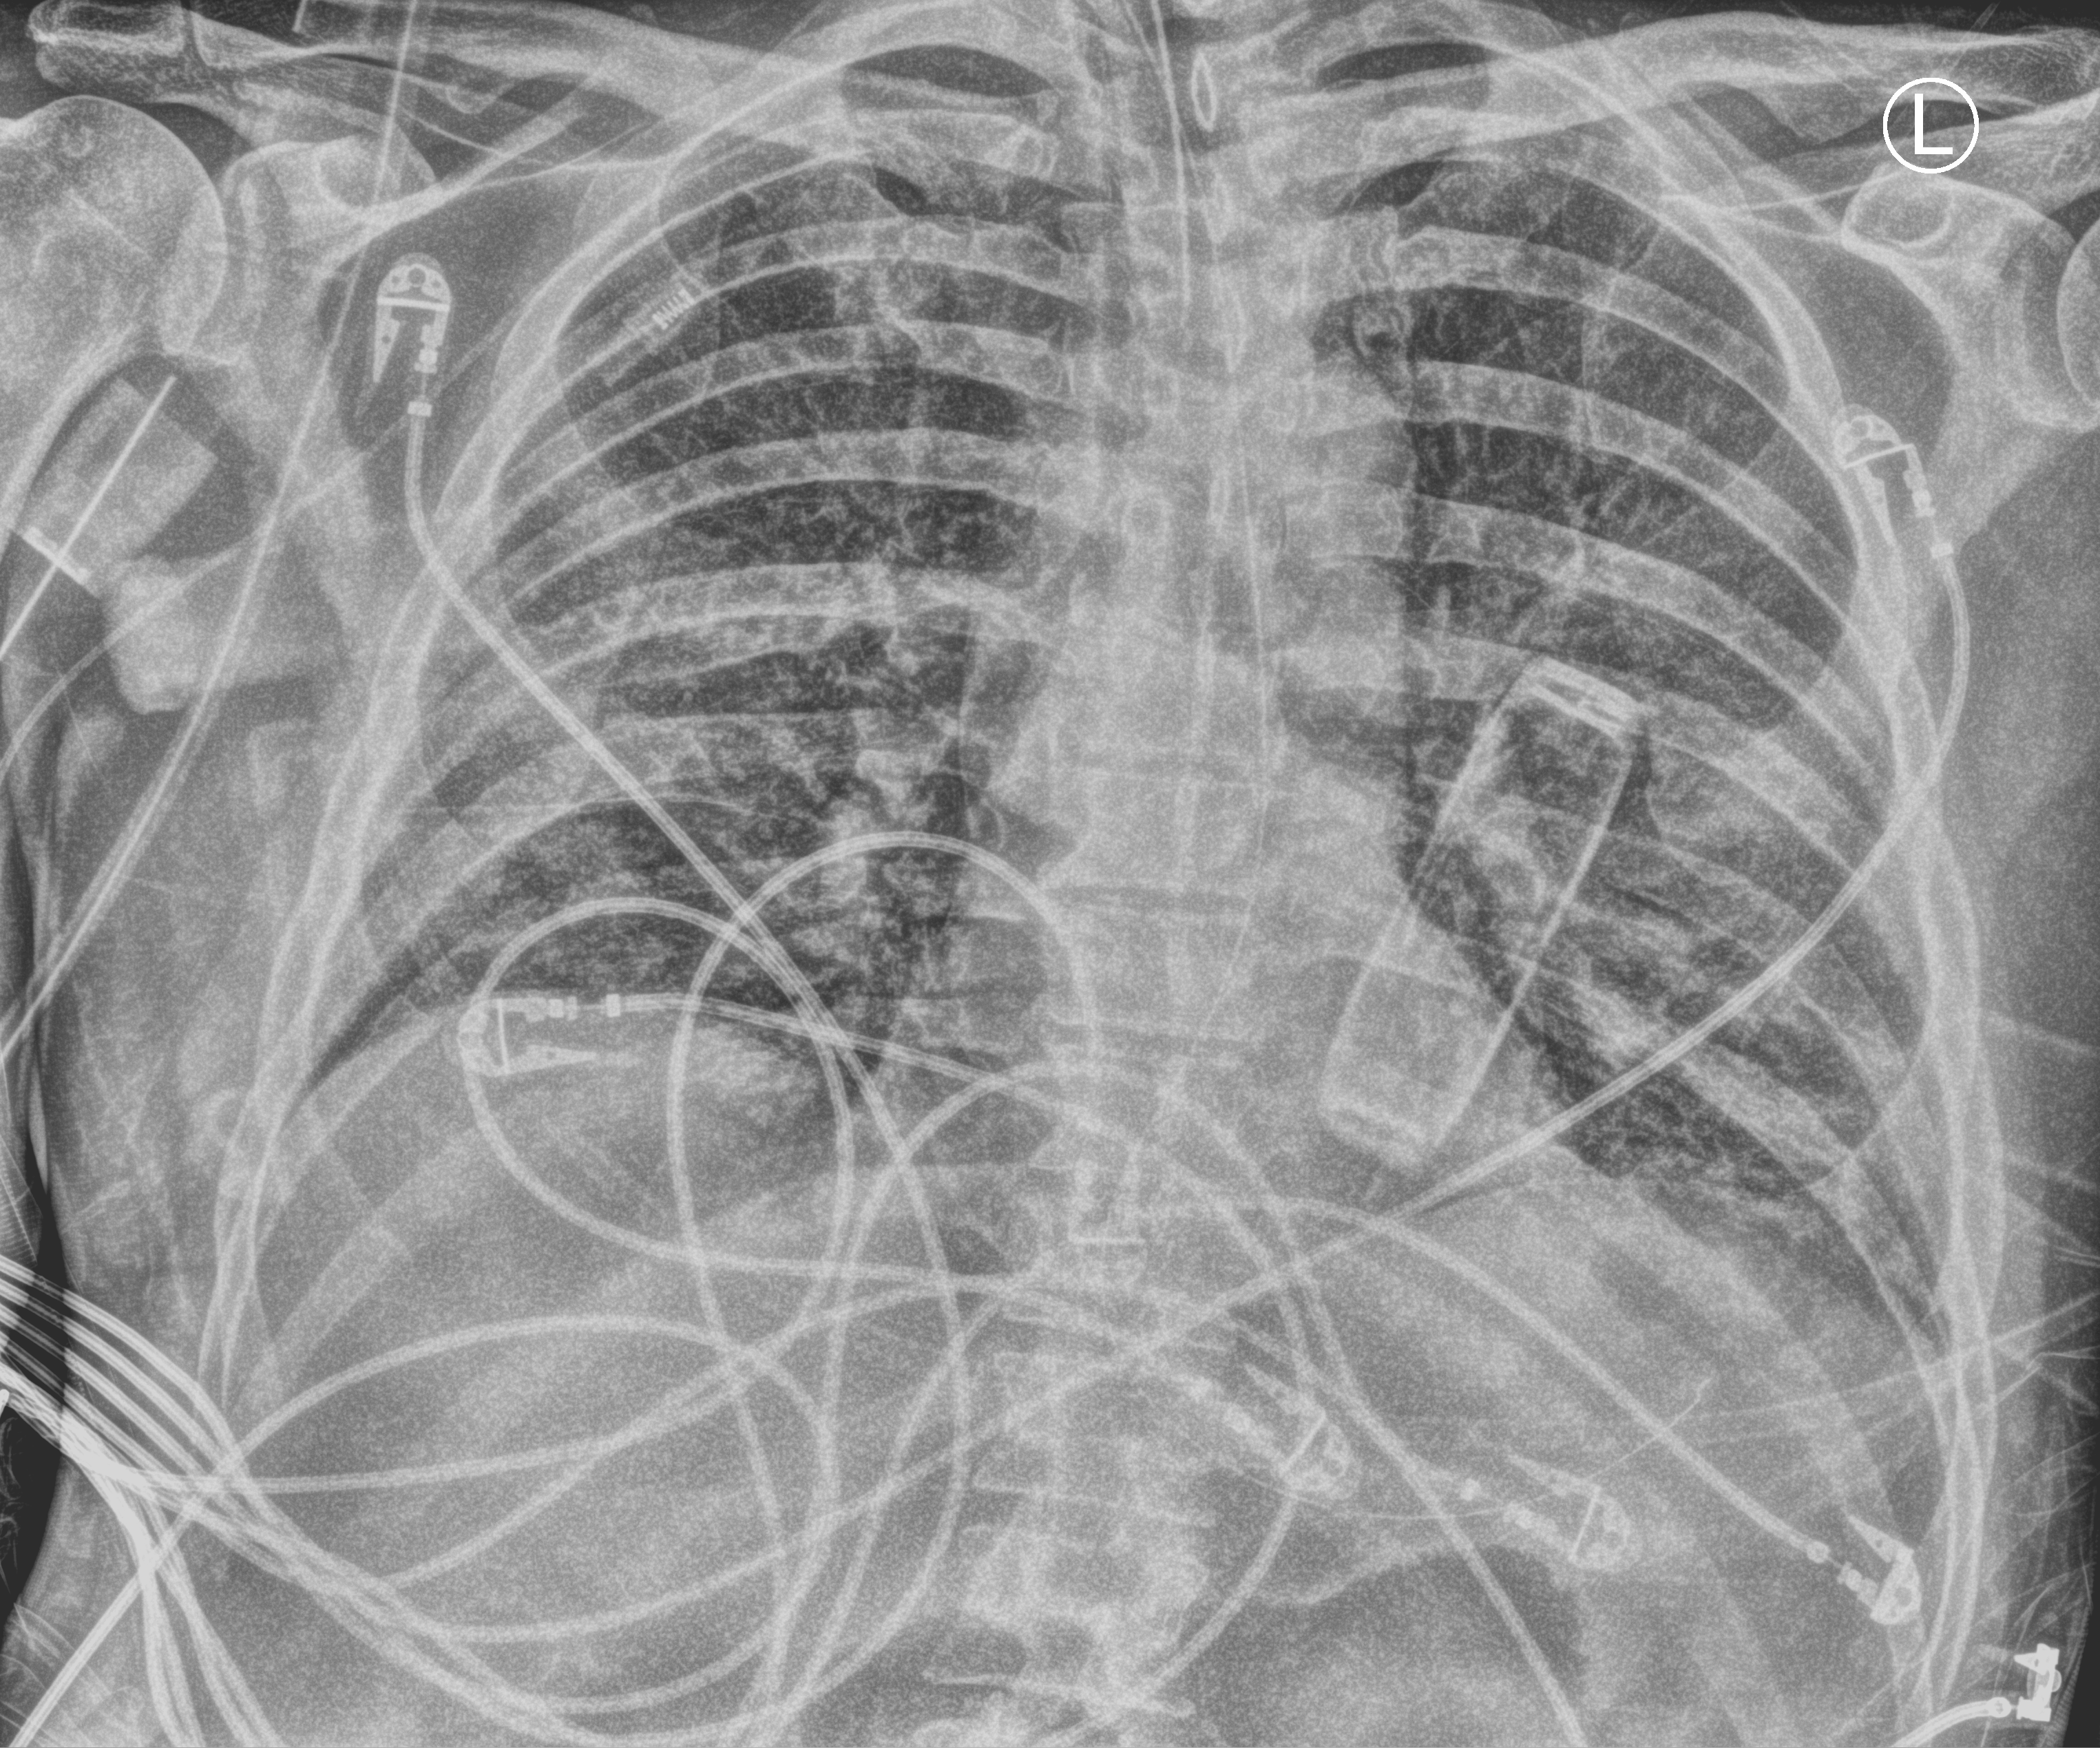
Chest X-ray (portable), anteroposterior (AP) projection. Patient hospitalised with COVID-19; male, aged 60–74 years.
From the hospital-stay record, not from the radiograph (when in the stay this image was taken is not recorded):
- admitted to intensive care during this hospital stay: yes
- smoking status (admission record): never
- mechanically ventilated during this hospital stay: yes